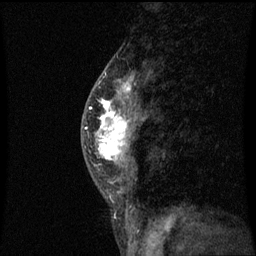
Breast MRI (dynamic contrast-enhanced), one sagittal slice. Dynamic contrast-enhanced series, image 2 of 3 at this slice position (ordered by acquisition). 1.5 T. TE 4.2 ms, TR 8.9 ms. 2 mm slice thickness. 256 × 256 image matrix, field of view 200 × 200 mm. Female patient, age 50 years. Case-level facts recorded for this patient, not image findings: setting: breast cancer imaged before/during neoadjuvant chemotherapy; receptor status: triple-negative.
Outlined on this slice (semi-automatically segmented with operator editing):
- analysis volume of interest (the breast-tissue region the enhancement analysis was run in; not a lesion): bounding box (x1, y1, x2, y2) in pixels: (84, 80, 145, 171)
- tumour enhancement mask (voxels above the 70 % enhancement threshold inside the analysis volume of interest): (84, 82, 131, 161)